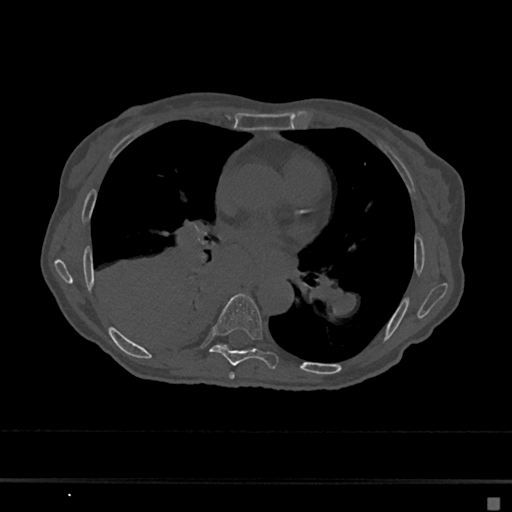
CT including the spine, one axial slice. Slice 368 of 797 in the series (ordered by position). Reconstruction kernel Br40s/3. Bone window (W 1800 / L 400 HU). 0.5 mm slice thickness. 512 × 512 image matrix, field of view 360 × 360 mm. Female patient, age 68 years. From the clinical record (not read from this slice): primary cancer: renal.
Annotated regions visible in this slice (semi-automatic segmentation, software-assisted and operator-edited):
- T6 vertebra: box from (x=229, y=372) to (x=235, y=379) px
- T7 vertebra: (x=209, y=294)–(x=279, y=369)